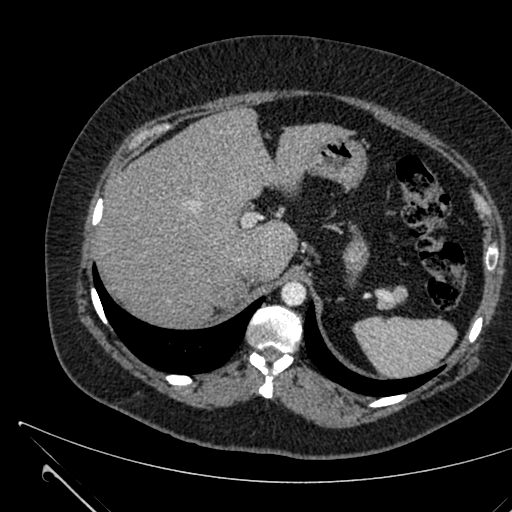
Contrast-enhanced abdominal CT, one axial slice. Slice 487 of 731 in the series (ordered by position). Intravenous contrast given. Soft-tissue window (W 400 / L 40 HU). 512 × 512 image matrix, field of view 376 × 376 mm. Patient: female, 36 years. Case-level facts recorded for this patient, not image findings: diagnosis: adrenocortical carcinoma; tumour side: right adrenal; tumour size at pathology: 10 cm; Ki-67 index: 20 %; stage (as recorded): 4.
Annotated regions visible in this slice (semi-automatic segmentation, software-assisted and operator-edited):
- mass: bounding box <227,281,246,306> (left, top, right, bottom; pixels)